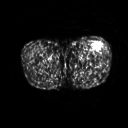
FDG PET of an extremity soft-tissue mass (from a PET/CT study), one axial slice. Position 220 of 267 along the scan axis. 128 × 128 image matrix, field of view 500 × 500 mm. Patient: male, 64 years. Case-level facts recorded for this patient, not image findings: histological type: extraskeletal osteosarcoma; grade: high; site of the primary tumour: thigh.
Outlined on this slice (expert contour drawn on MRI and transferred to this co-registered scan by the dataset authors):
- gross tumour volume (mass): bounding box <94,43,101,51> (left, top, right, bottom; pixels)